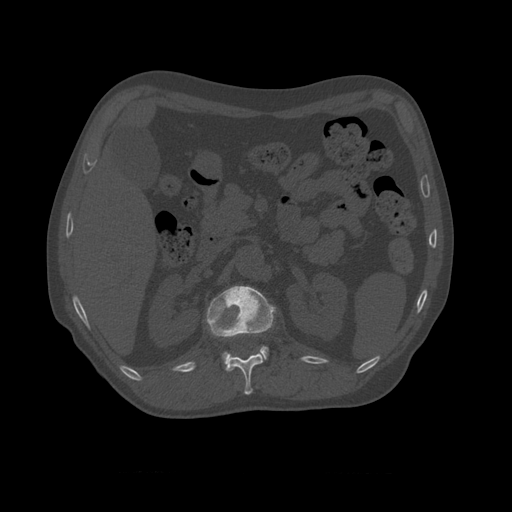
CT including the spine, one axial slice; reconstruction kernel STANDARD; 120 kVp; bone window (W 1800 / L 400 HU); 1.25 mm slice thickness; 512 × 512 image matrix, field of view 405 × 405 mm. Patient age 75 years. Case-level facts recorded for this patient, not image findings: primary cancer: prostate.
Annotated regions visible in this slice (semi-automatic segmentation, software-assisted and operator-edited):
- L1 vertebra: bounding box <206,286,277,370> (left, top, right, bottom; pixels)
- T10 vertebra: <259,346,270,361>
- T11 vertebra: <226,353,264,395>